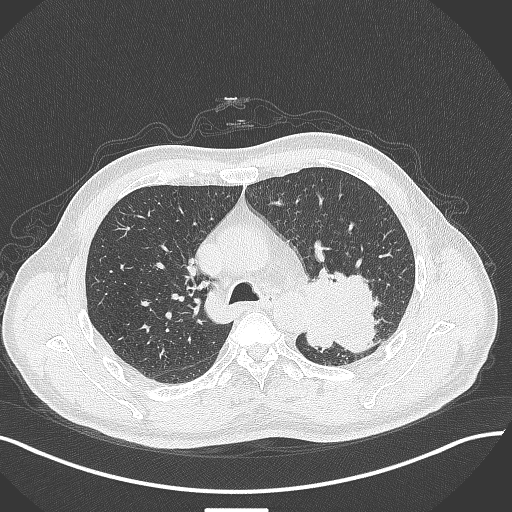
Chest CT, one axial slice; position 289 of 429 along the scan axis; reconstruction kernel B70f; lung window (W 1500 / L -600 HU); 1 mm slice thickness; 512 × 512 image matrix, field of view 400 × 400 mm. Male patient, age 55 years. From the clinical record (not read from this slice): clinical TNM (as recorded): T3 N0 M1c; histopathological grade: G3.
Outlined on this slice (bounding box drawn by a radiologist):
- lung tumour (recorded histology: adenocarcinoma): bounding box <305,264,381,353> (left, top, right, bottom; pixels)